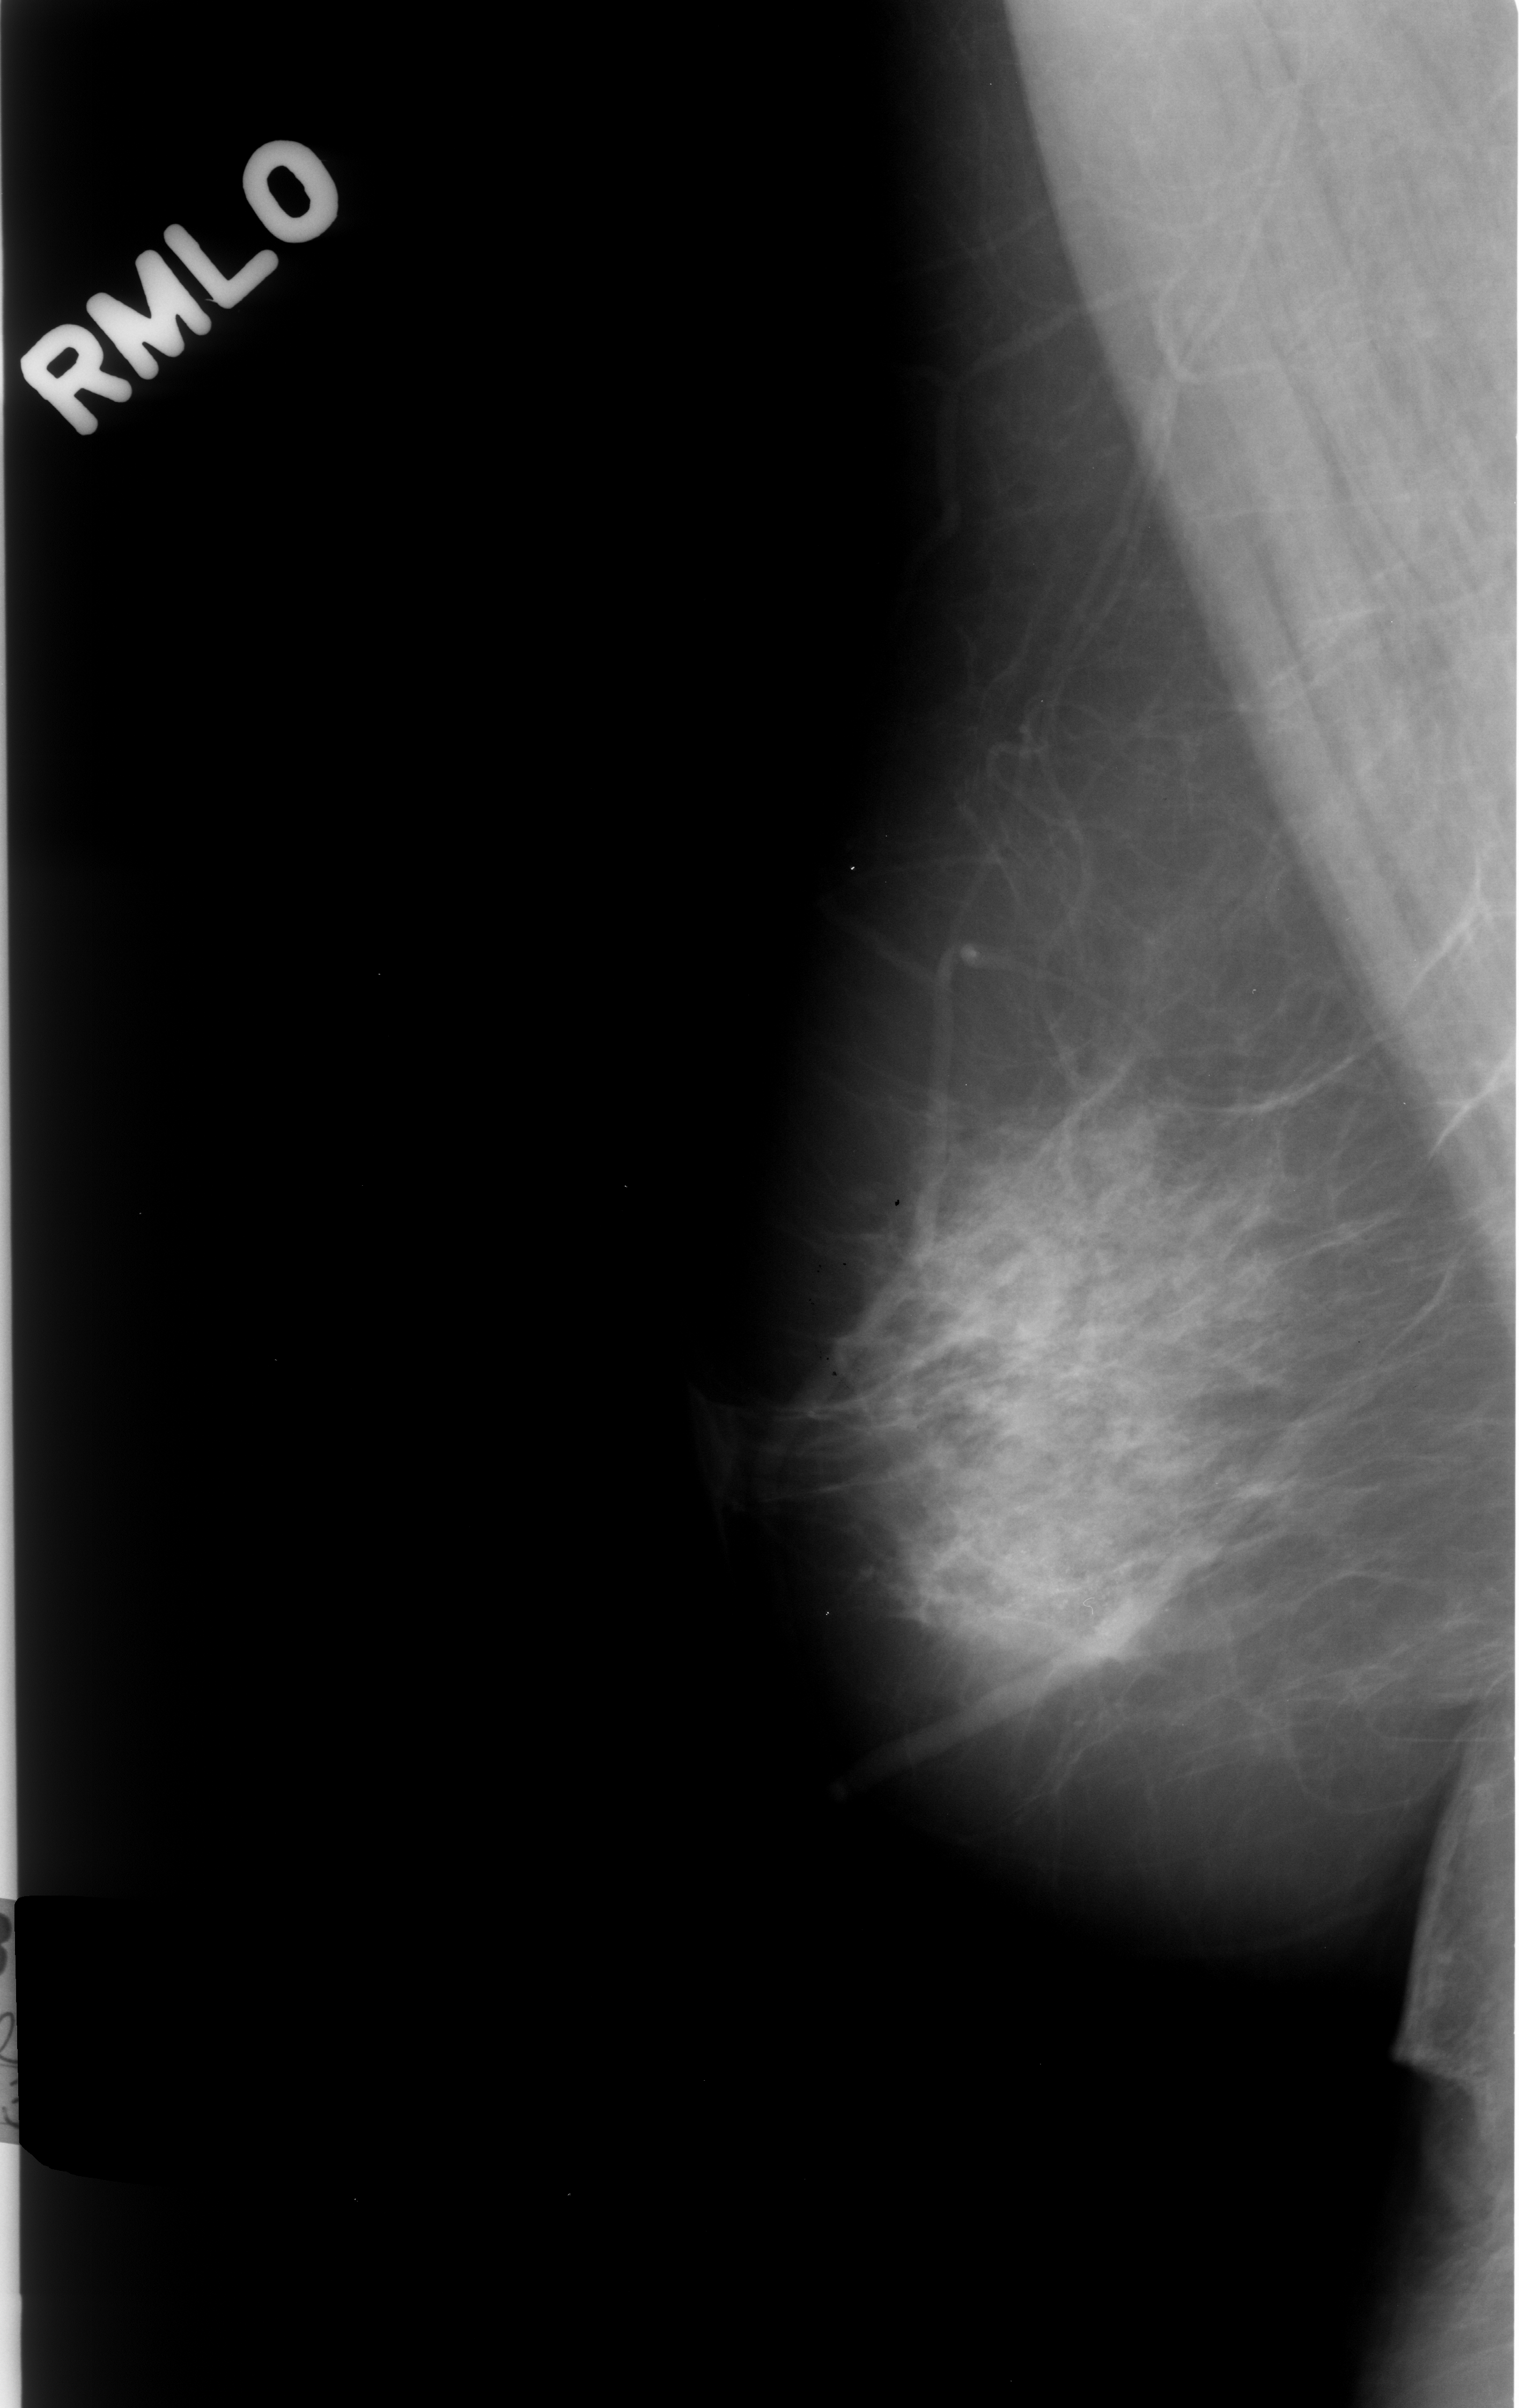
Mammogram (digitized film), right breast, MLO view, breast composition: scattered fibroglandular densities (BI-RADS density category 2 of 4).
Calcifications, morphology amorphous, distribution clustered; BI-RADS assessment category 4; subtlety rating 3 on a 1 (subtle) to 5 (obvious) scale; pathology (as recorded): benign.